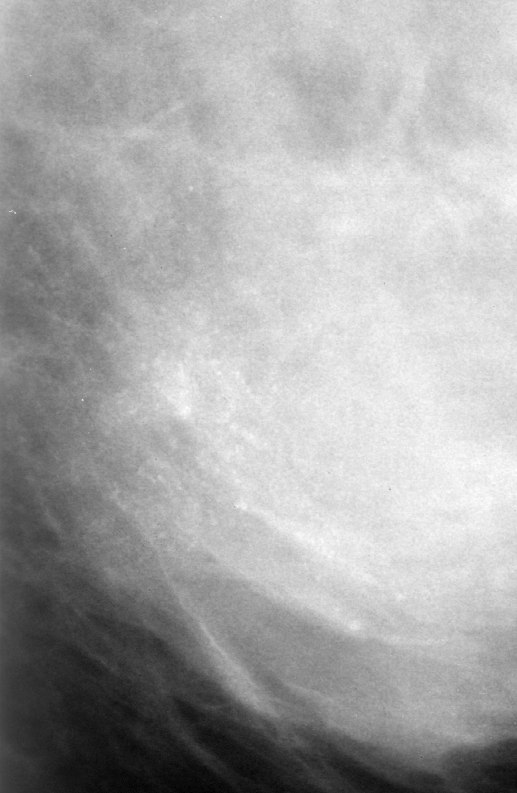
Crop from a digitized film mammogram around one marked abnormality; left breast; MLO view.
Finding: calcifications, morphology pleomorphic, distribution clustered; BI-RADS assessment category 4; pathology (as recorded): malignant.